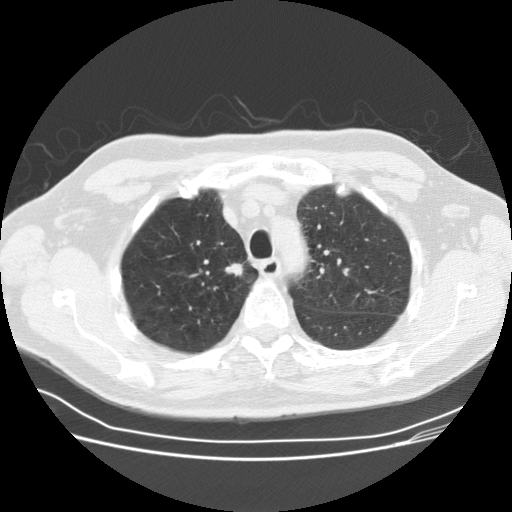
Axial slice from a low-dose chest CT screening exam. Third screening round (two years after baseline). Lung window (W 1500 / L -600 HU). 2.5 mm slice thickness. 512 × 512 image matrix. Male participant, aged 69 years at enrolment.
- Lesion marked by an expert reader, bounding box [x1, y1, x2, y2] px = [220, 256, 257, 289].
- The exam's reader record, not a measurement of the box and not confirmed to be the same lesion: non-calcified nodule or mass ≥4 mm, right upper lobe, 12 × 10 mm, spiculated (stellate) margins, soft tissue attenuation, pre-existing on the prior screen: yes; interval growth: yes.
- Official screen result: positive, other.